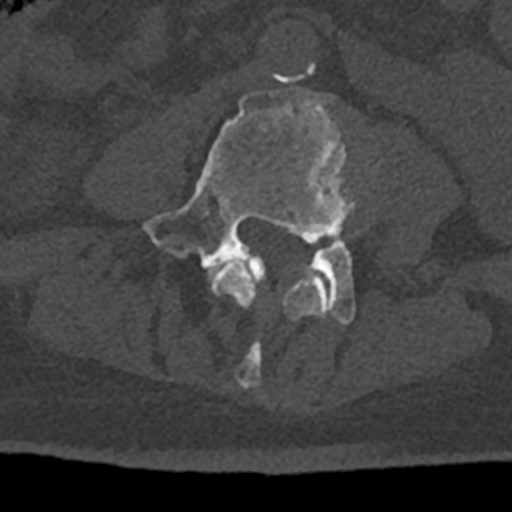
CT including the spine, one axial slice; reconstruction kernel Br40s/3; 120 kVp; bone window (W 1800 / L 400 HU); 512 × 512 image matrix, field of view 160 × 160 mm. Patient: male, 74 years. Case-level facts recorded for this patient, not image findings: primary cancer: renal.
Outlined on this slice (semi-automatically segmented with operator editing):
- L3 vertebra: bounding box (x1, y1, x2, y2) in pixels: (212, 259, 331, 389)
- L4 vertebra: (141, 88, 366, 325)